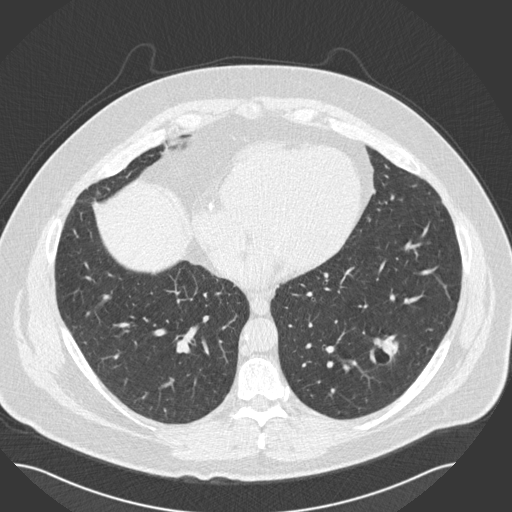
Axial slice from a low-dose chest CT screening exam. Second annual screen. Lung window (W 1500 / L -600 HU). 2 mm slice thickness. 120 kVp. Slice 91 of 162 in the series. Male, age 57 years at enrolment. Current smoker at enrolment.
Expert-annotated lung lesion, bounding box [x1, y1, x2, y2] px = [351, 325, 417, 377]. Screening reader's record for this exam (one nodule recorded; not confirmed to be the boxed lesion): non-calcified nodule or mass ≥4 mm, left lower lobe, 19 × 15 mm, pre-existing on the prior screen: yes; interval growth: no. Official screen result: positive, no significant change: stable abnormalities potentially related to lung cancer, unchanged since the prior screening exam. Later outcome: lung cancer diagnosed 434 days after this screen (after the third annual screen) — squamous cell carcinoma, NOS, left lower lobe, moderately differentiated (G2), stage IA (AJCC 6th edition), 22 mm at pathology.